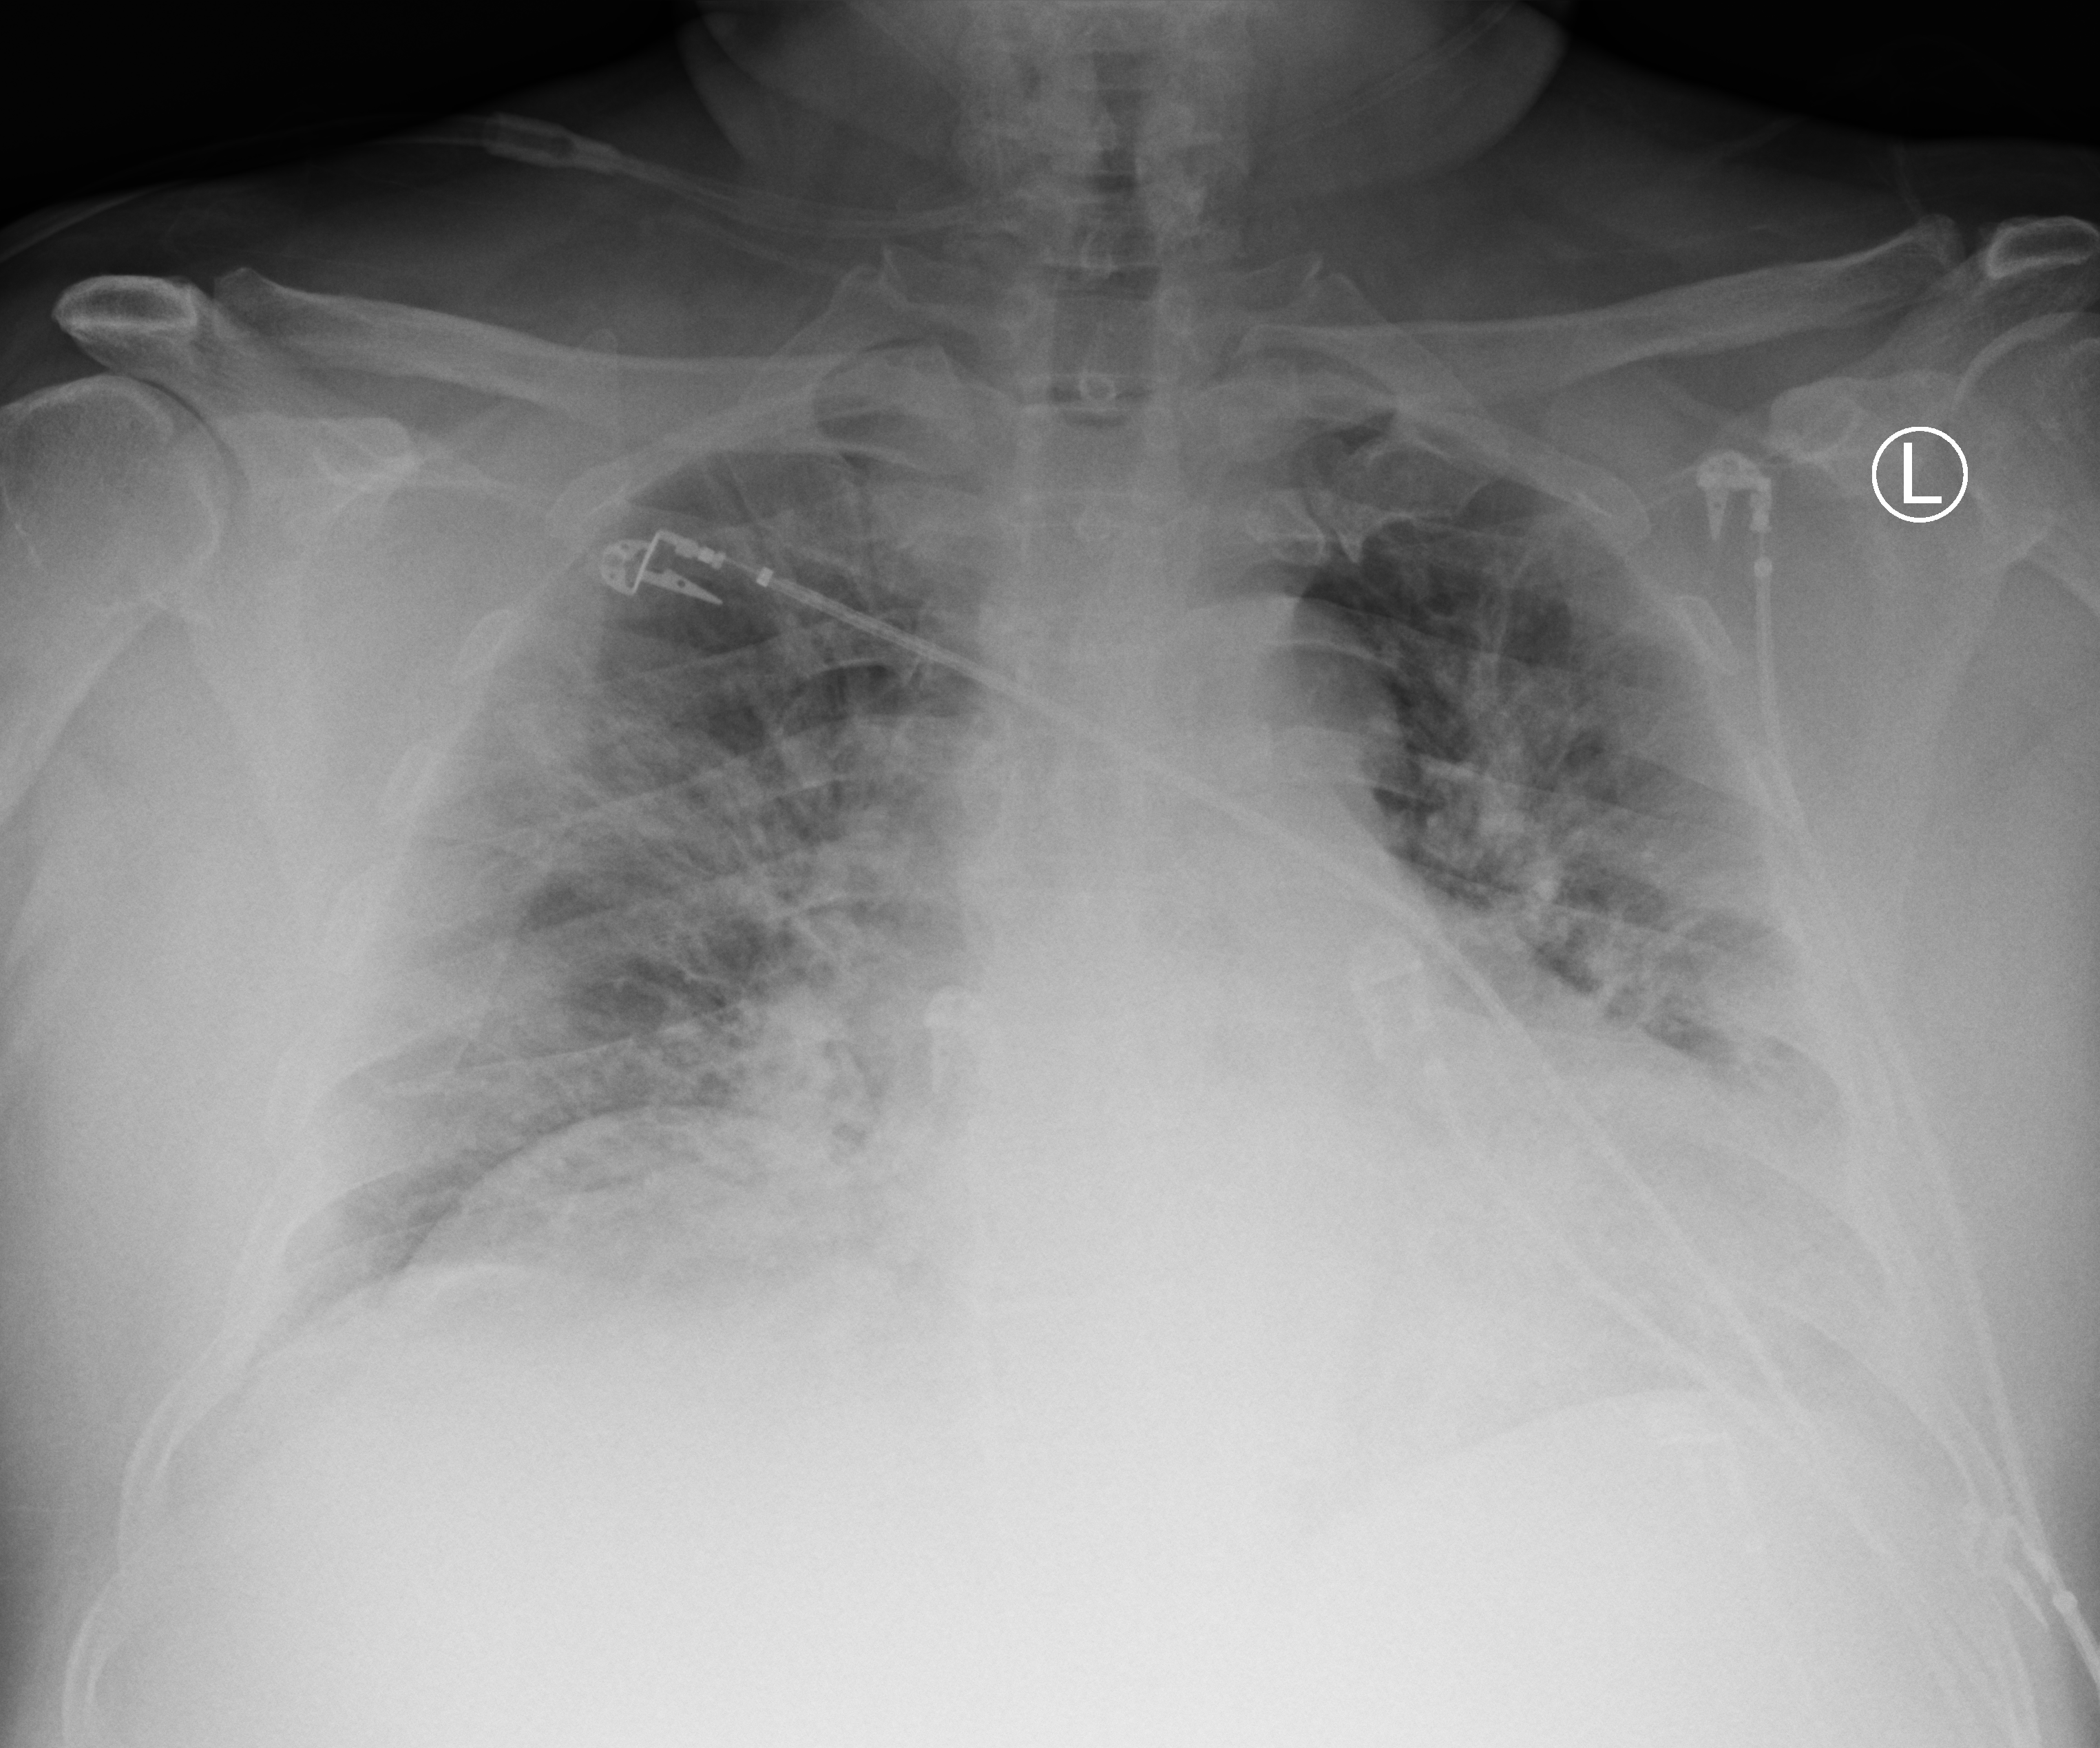
Chest X-ray (portable), anteroposterior (AP) projection. Male patient hospitalised with COVID-19, age 60–74 years.
Admission-level facts for this patient (not findings on this image; timing relative to this image not recorded):
- mechanically ventilated during this hospital stay: yes
- length of hospital stay: 28 days
- admitted to intensive care during this hospital stay: yes